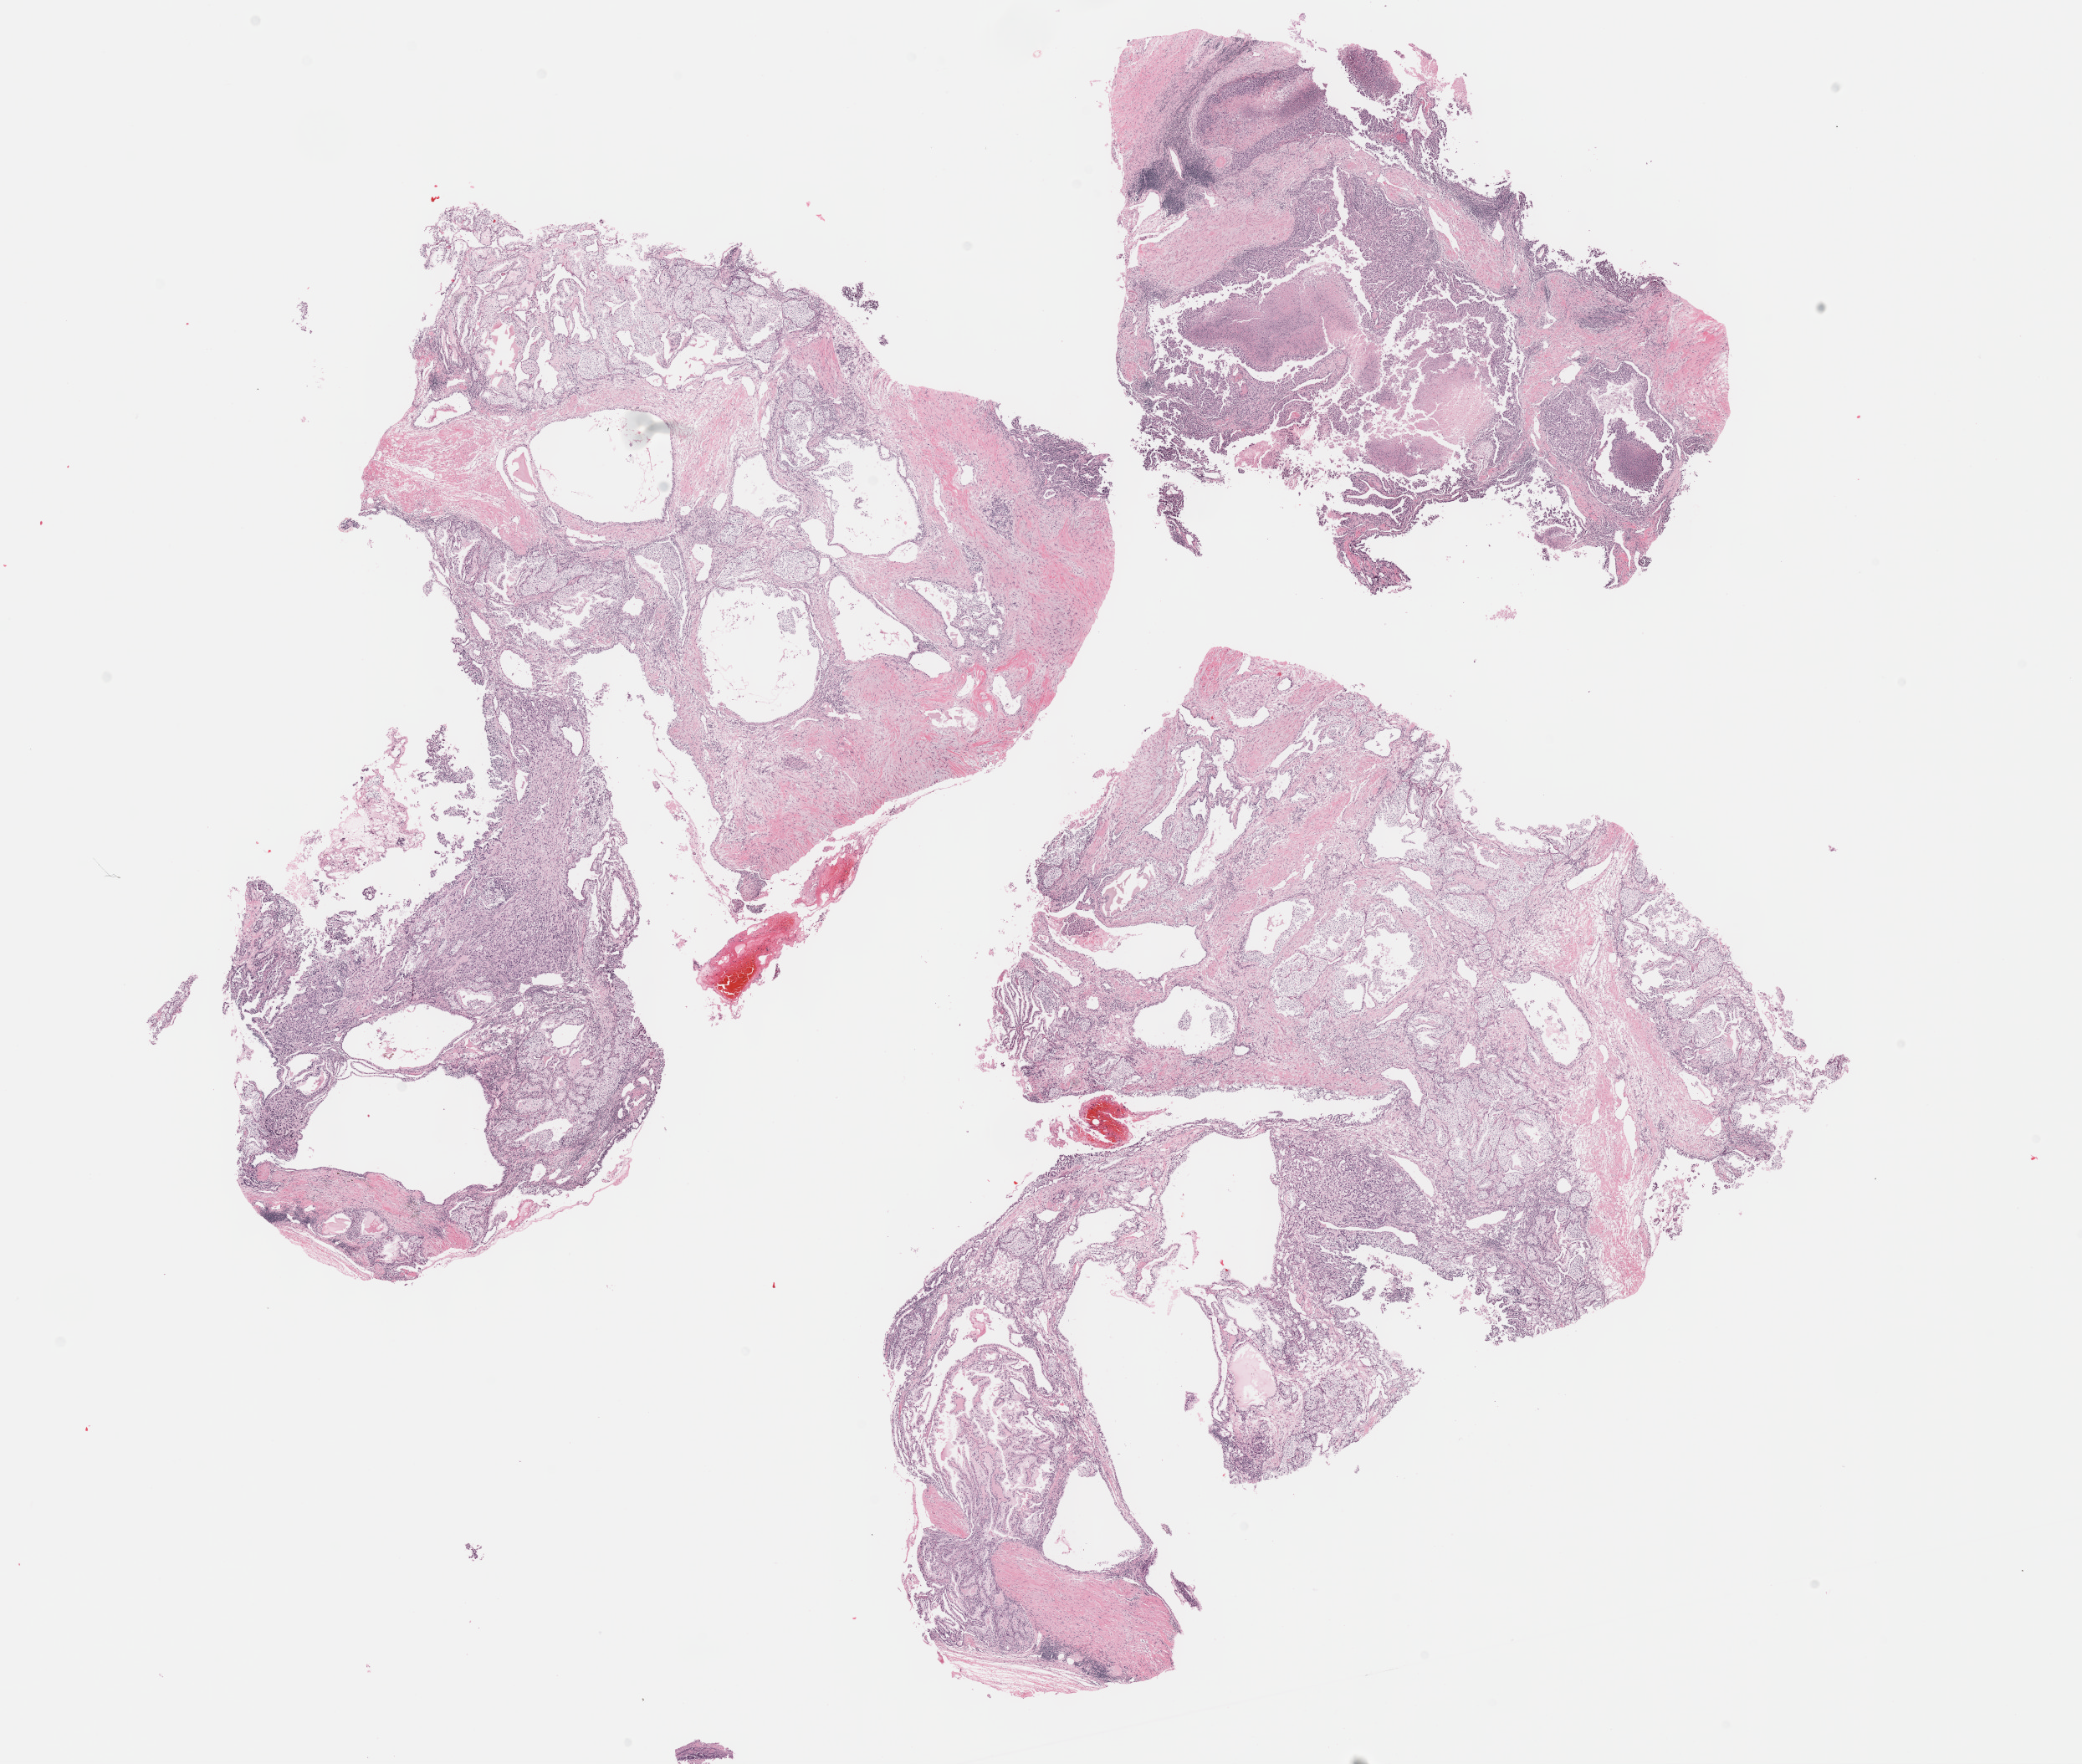
H&E-stained whole-slide image, whole scanned area (about 20.1 x 17.1 mm) shown as a low-resolution overview, FFPE section, sample: primary tumour, kidney. Male, age 37 years at initial diagnosis. Histologic grade: G3 (poorly differentiated).
• laterality: right
• lymph nodes positive (case pathology): 3 of 10 examined
• AJCC pathologic stage: III
• pathologic diagnosis: Clear cell adenocarcinoma, NOS